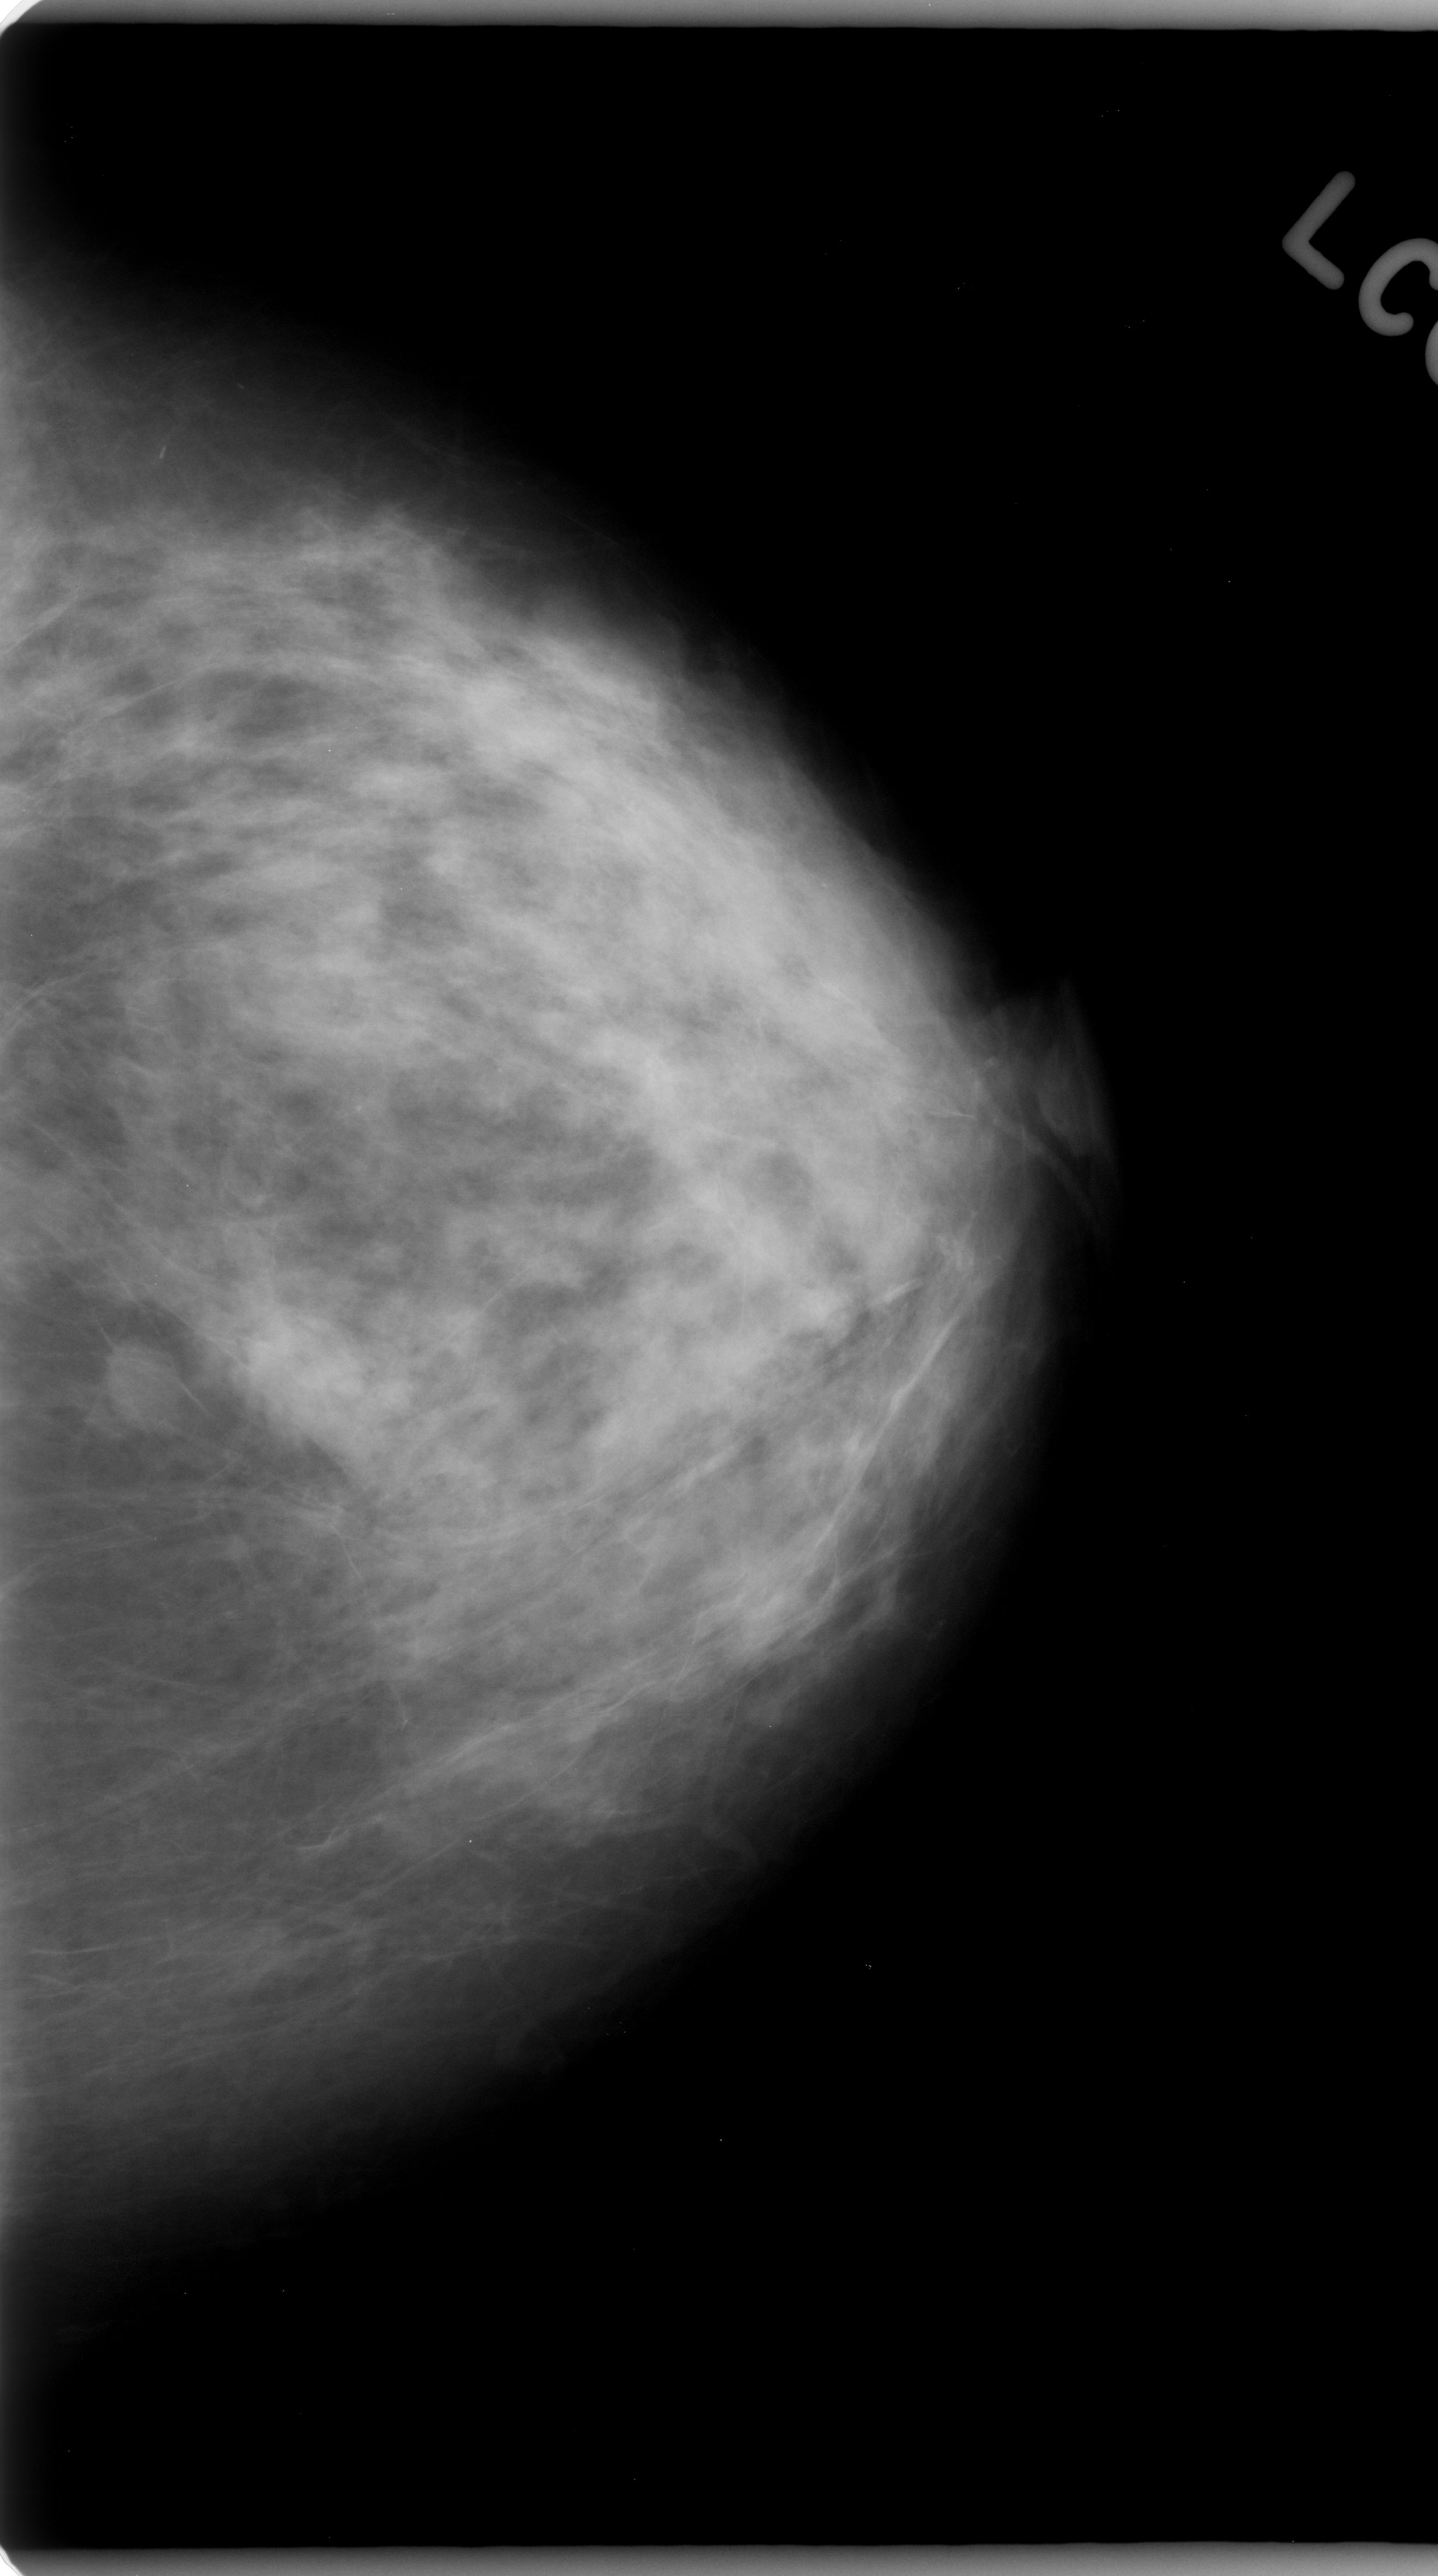
Scanned film-screen mammogram; left breast; craniocaudal (CC) view; breast composition: scattered fibroglandular densities (BI-RADS density category 2 of 4); 1438 × 2576 image matrix.
Expert-marked regions of interest on this film, with their recorded descriptors:
- mass, shape oval, margins circumscribed; BI-RADS assessment category 3; pathology (as recorded): benign: bounding box [x1, y1, x2, y2] px = [99, 1337, 180, 1433]